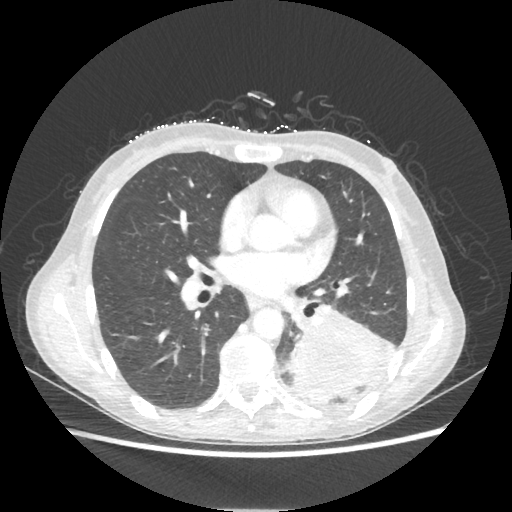
Chest CT, one axial slice. Slice 108 of 221 in the series (ordered by position). 80 kVp. Lung window (W 1500 / L -600 HU). 1.25 mm slice thickness. 512 × 512 image matrix, field of view 360 × 360 mm. Female patient, age 53 years. Case-level facts recorded for this patient, not image findings: clinical TNM (as recorded): T3 N0 M0.
Annotated regions visible in this slice (rectangle marked by the reading radiologist):
- lung tumour (recorded histology: adenocarcinoma): bounding box [x1, y1, x2, y2] px = [286, 310, 394, 405]